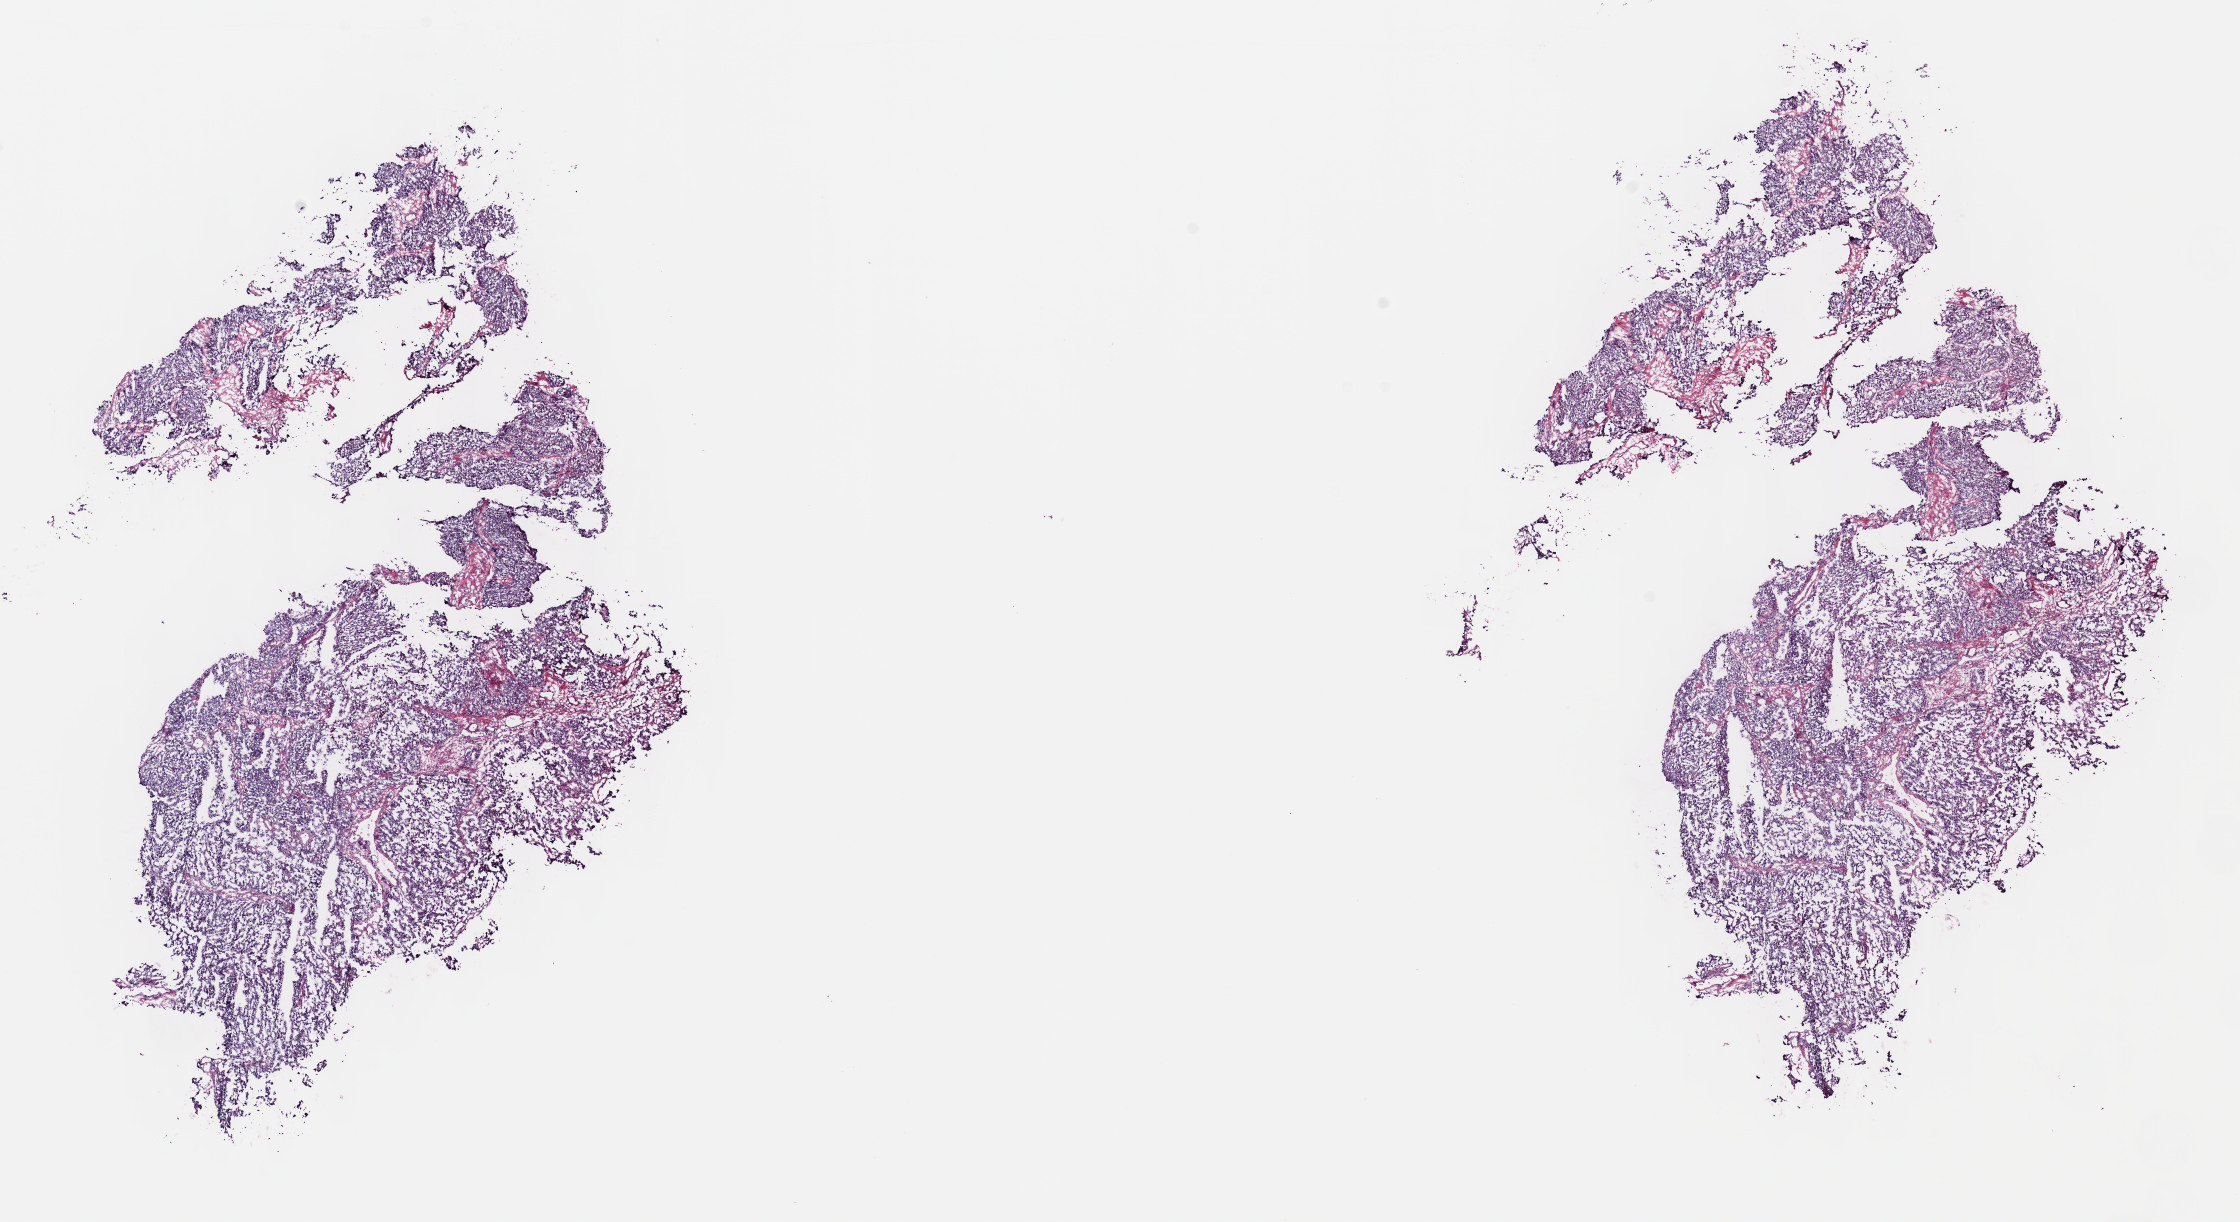
H&E whole-slide image — whole scanned area (about 18.1 x 9.9 mm, slide scanned at 40x) shown as a low-resolution overview; frozen section from the top of the tissue portion; primary tumour sample from the bladder. Male patient; age at initial diagnosis 63 years. Histologic grade: high grade. Slide review estimates, as recorded: tumour cells 100%, tumour nuclei 80%, normal cells 0%, stromal cells 0%, necrosis 0%. Infiltration values recorded for this section: lymphocyte infiltration 3%, monocyte infiltration 0%, neutrophil infiltration 0%.
* AJCC pathologic stage: III (7th edition)
* pathologic diagnosis: Transitional cell carcinoma